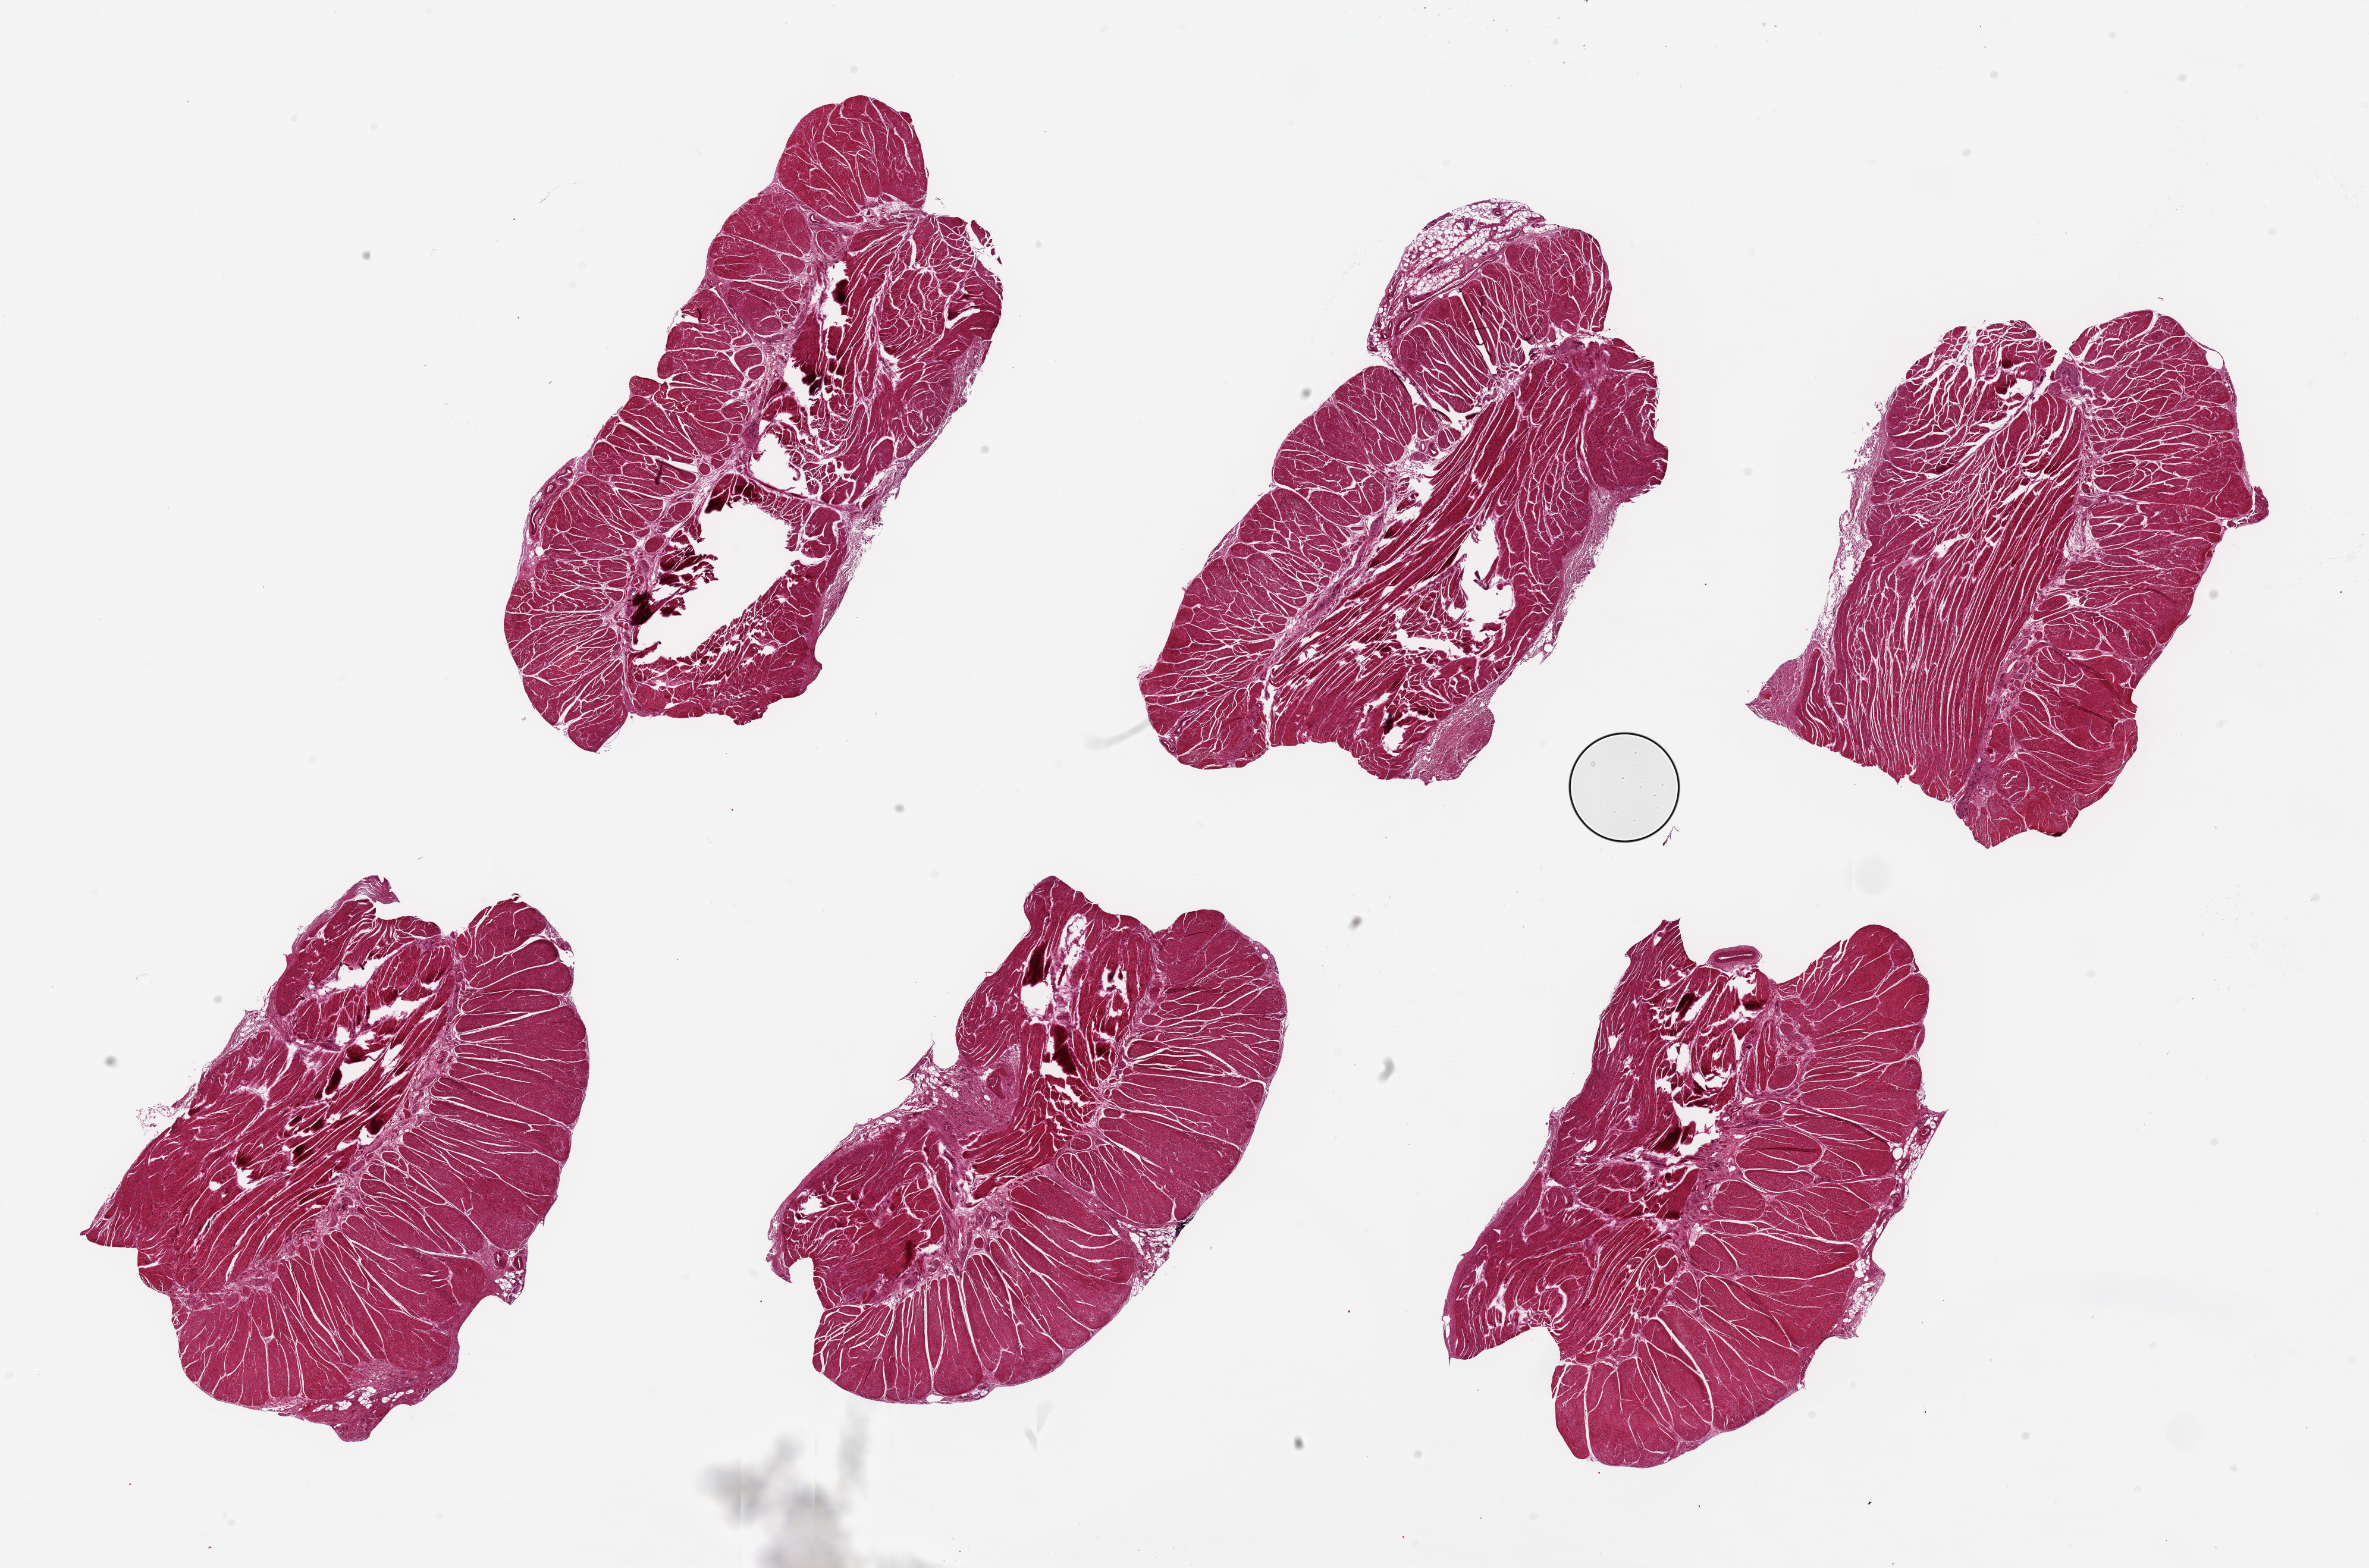
Whole-slide image, hematoxylin and eosin (H&E) stain, brightfield — low-resolution overview of the scanned area, about 31.5 x 20.9 mm. PAXgene-fixed, paraffin-embedded tissue. Section of esophageal muscle (target tissue). Tissue donor sample.
- review note (as recorded): 6 pieces, up to 9x4mm; all muscularis; good specimens